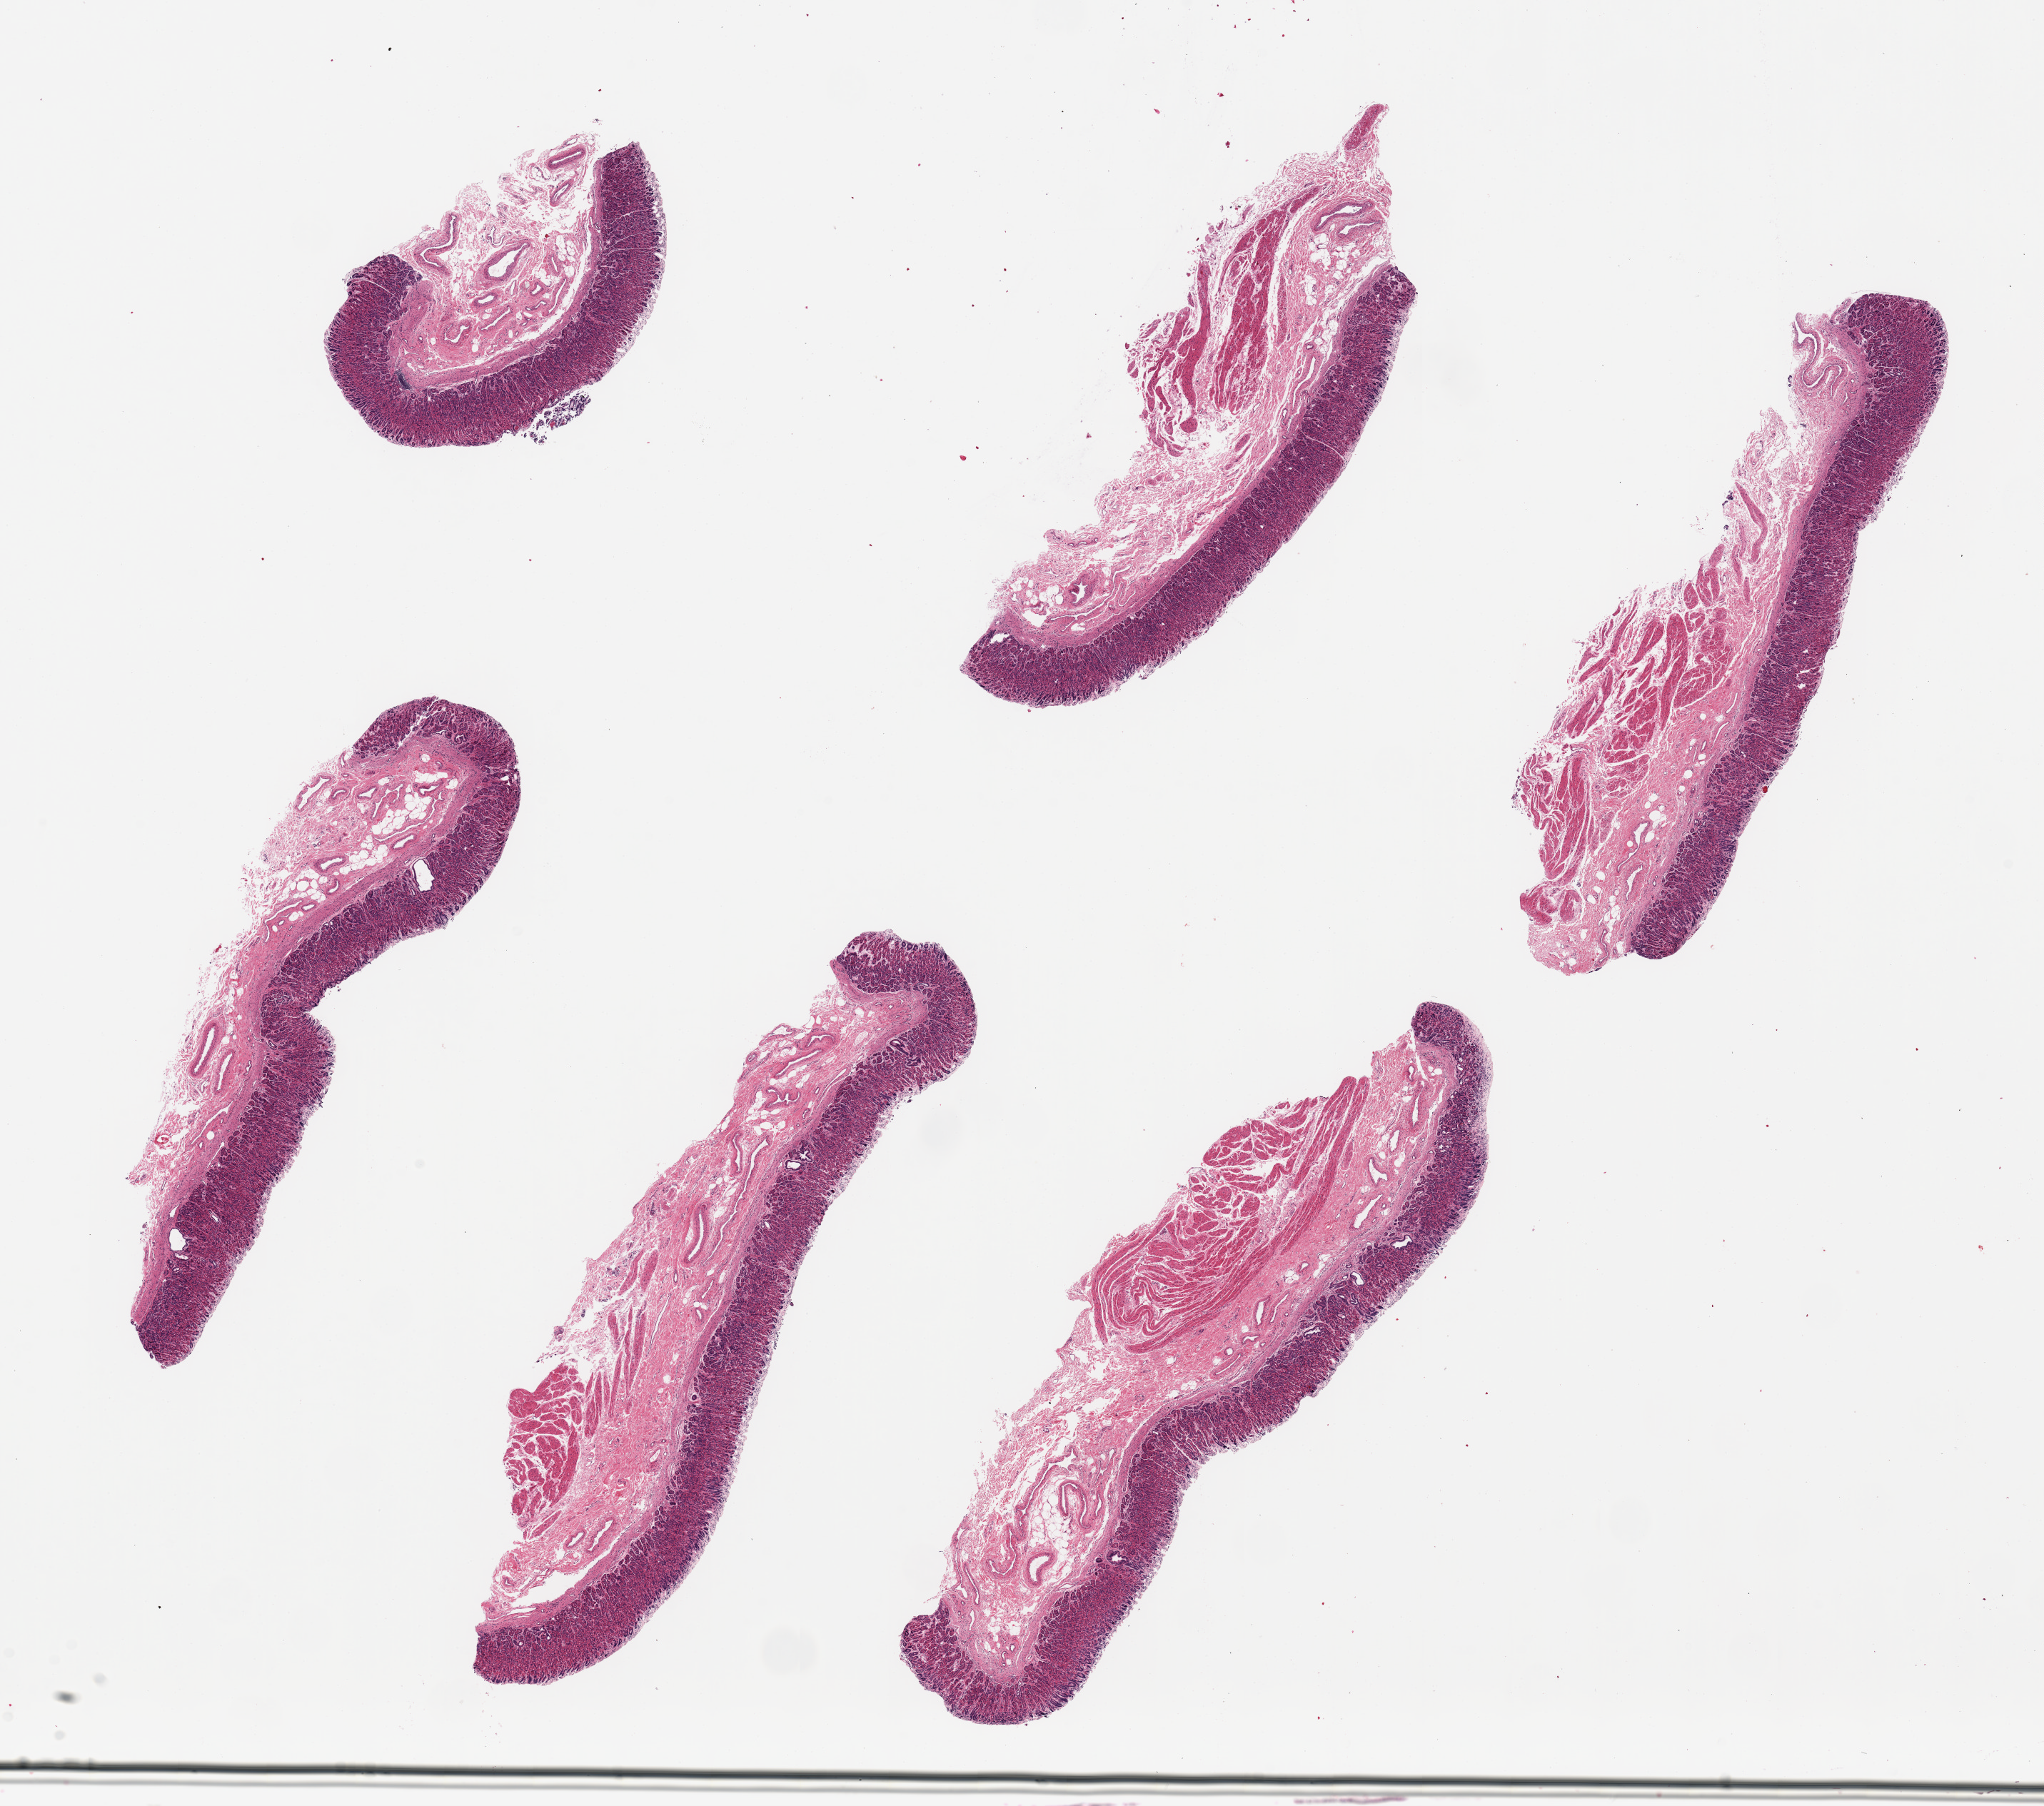
Digitized H&E-stained section, low-resolution overview of the scanned area, about 22.6 x 20.0 mm (slide scanned at 20x); PAXgene-fixed paraffin-embedded (PFPE) section; section of stomach (target tissue); tissue donor sample. Donor sex: male.
Review note (as recorded): 6 pieces ~9x2mm. Mucosa extremely well preserved, ~30-40% thickness.